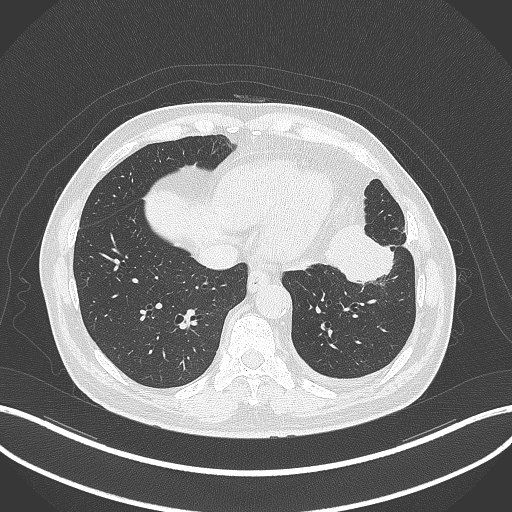
Chest CT, one axial slice. Position 100 of 230 along the scan axis. 120 kVp. Lung window (W 1500 / L -600 HU). 1 mm slice thickness. 512 × 512 image matrix, field of view 400 × 400 mm. Patient: male, 68 years. Case-level facts recorded for this patient, not image findings: clinical TNM (as recorded): T2b N0 M0.
Outlined on this slice (rectangle marked by the reading radiologist):
- lung tumour (recorded histology: squamous cell carcinoma): bounding box (x1, y1, x2, y2) in pixels: (323, 220, 398, 288)